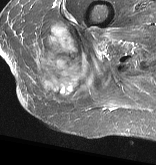
MRI of an extremity soft-tissue mass, one axial slice; position 16 of 57 along the scan axis; STIR; MR volume resampled by the dataset authors to the PET/CT grid (not the native acquisition matrix); 156 × 165 image matrix, field of view 152 × 161 mm. Female patient. From the clinical record (not read from this slice): histological type: epithelioid sarcoma with vascular differentiation; site of the primary tumour: right buttock.
Structures marked on this image (expert contour drawn on MRI and transferred to this co-registered scan by the dataset authors):
- gross tumour volume (mass): bounding box (x1, y1, x2, y2) in pixels: (33, 21, 107, 104)